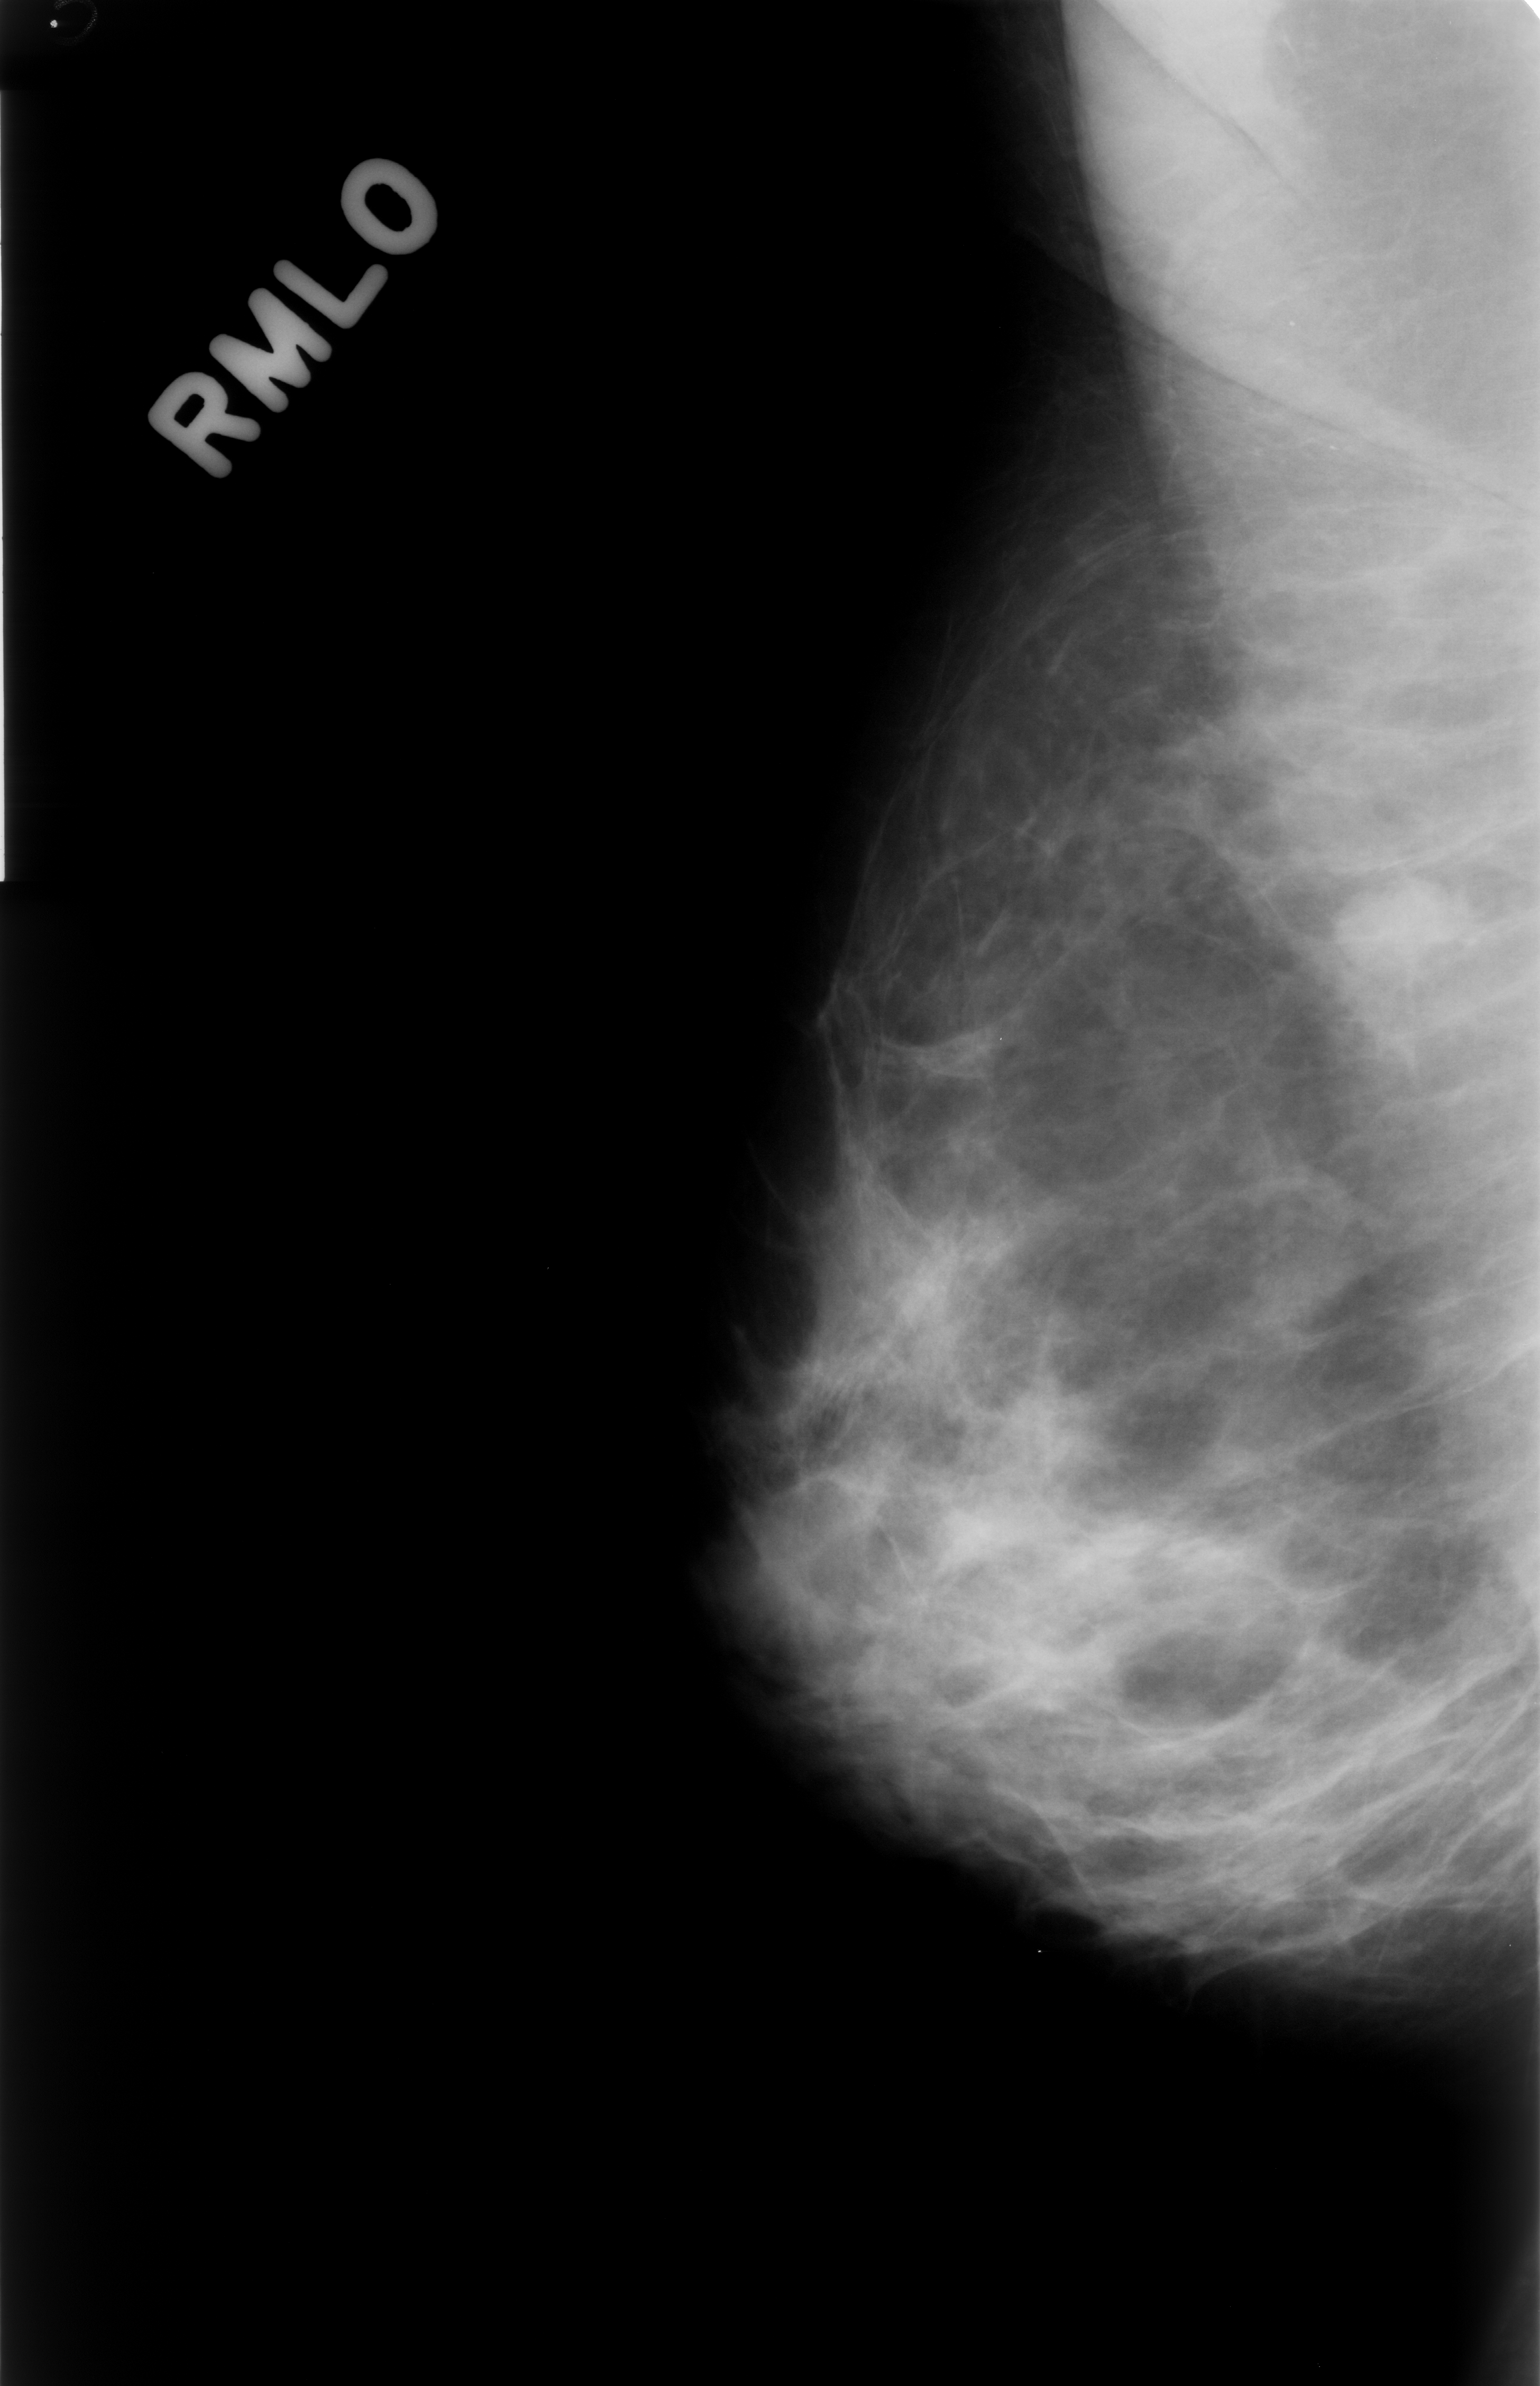
Digitized screen-film mammogram. Right breast. Mediolateral oblique (MLO) view. BI-RADS breast density category 3 (scale 1–4). 1540 × 2386 image matrix.
Expert-marked regions of interest on this film, with their recorded descriptors:
- mass, shape oval, margins circumscribed; BI-RADS assessment category 4; pathology (as recorded): benign: box from (x=1303, y=872) to (x=1478, y=1012) px